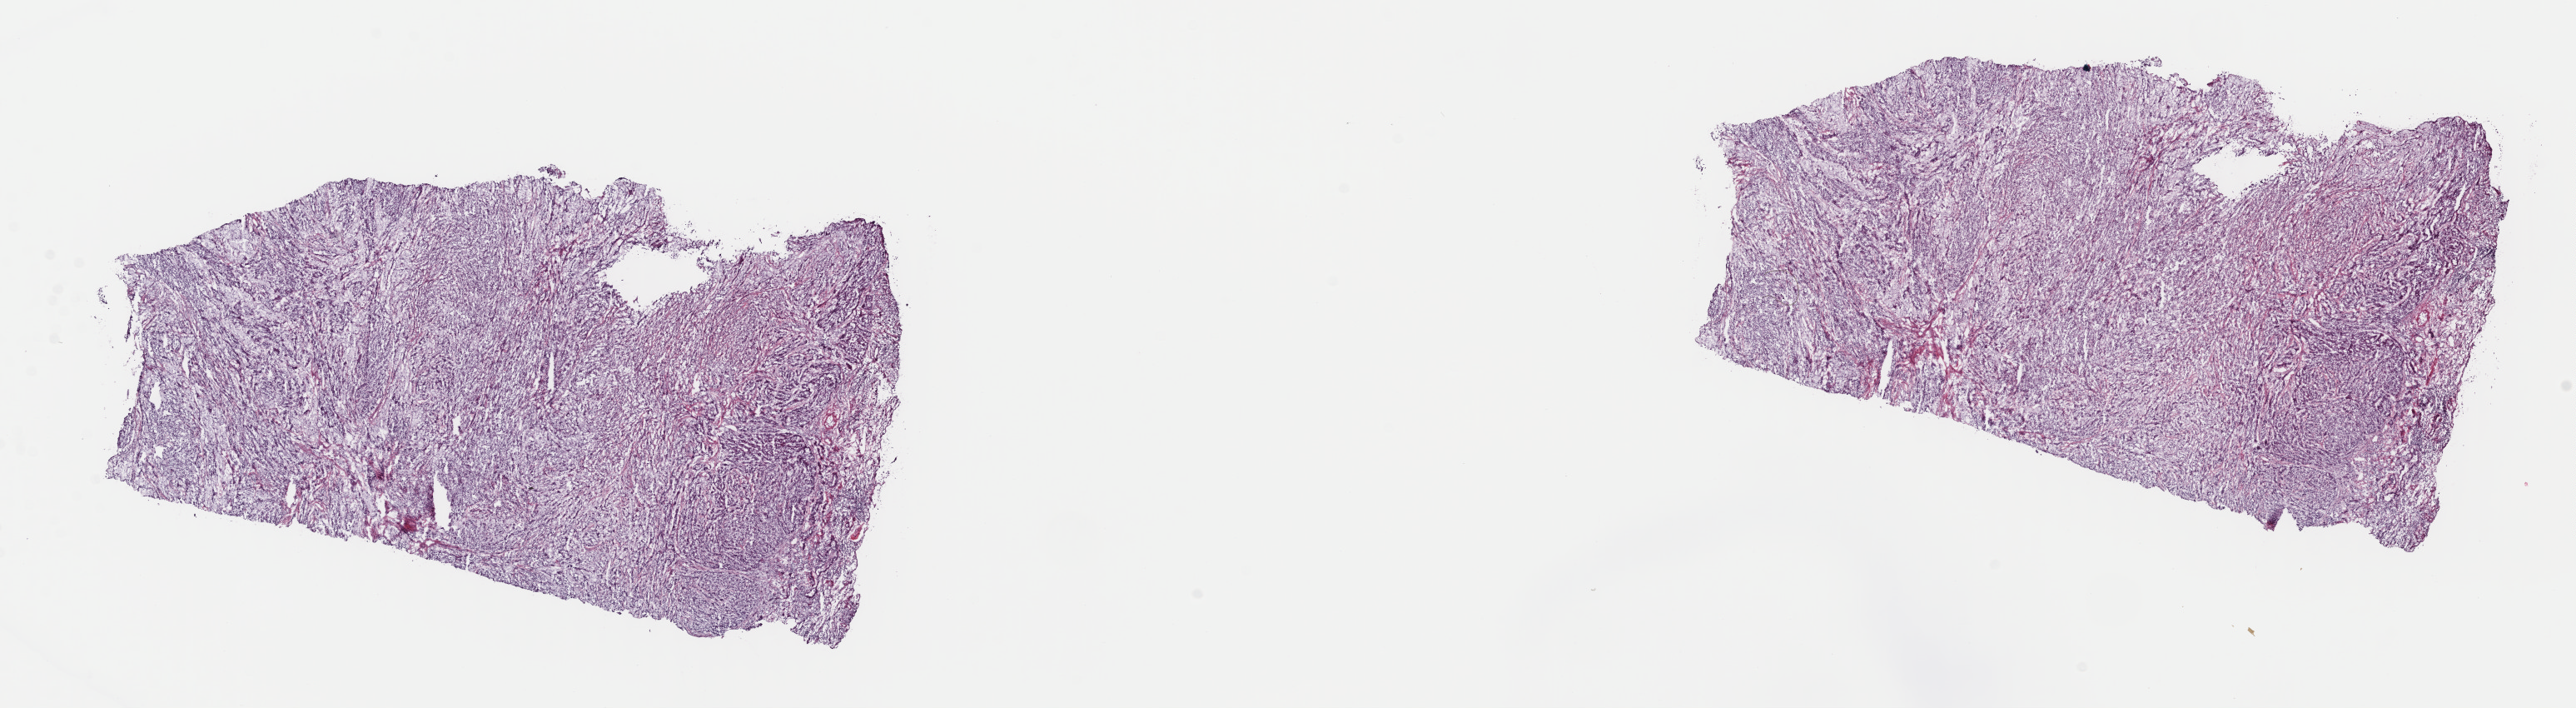
H&E whole-slide image — a low-resolution overview of the entire scanned area, about 24.4 x 6.7 mm; frozen section from the top of the tissue portion; sample: primary tumour, kidney. Female, age 60 years at initial diagnosis. Pathologist review of this section (percent, as recorded): tumour cells 78%, tumour nuclei 80%, normal cells 0%, stromal cells 20%, necrosis 2%. Infiltration values recorded for this section: lymphocyte infiltration 5%, monocyte infiltration 5%, neutrophil infiltration 0%.
TNM: T1a NX M0. Diagnosis: Papillary adenocarcinoma, NOS. AJCC pathologic stage: I (7th edition).